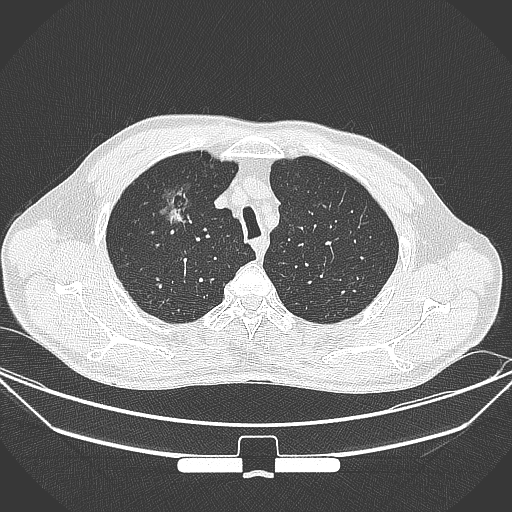
Chest CT, one axial slice. Slice 282 of 355 in the series (ordered by position). 120 kVp. Lung window (W 1500 / L -600 HU). 1 mm slice thickness. 512 × 512 image matrix. Patient: male, 67 years. Case-level facts recorded for this patient, not image findings: clinical TNM (as recorded): T1c N0 M0.
Structures marked on this image (bounding box drawn by a radiologist):
- lung tumour (recorded histology: adenocarcinoma): bounding box [x1, y1, x2, y2] px = [157, 178, 199, 230]